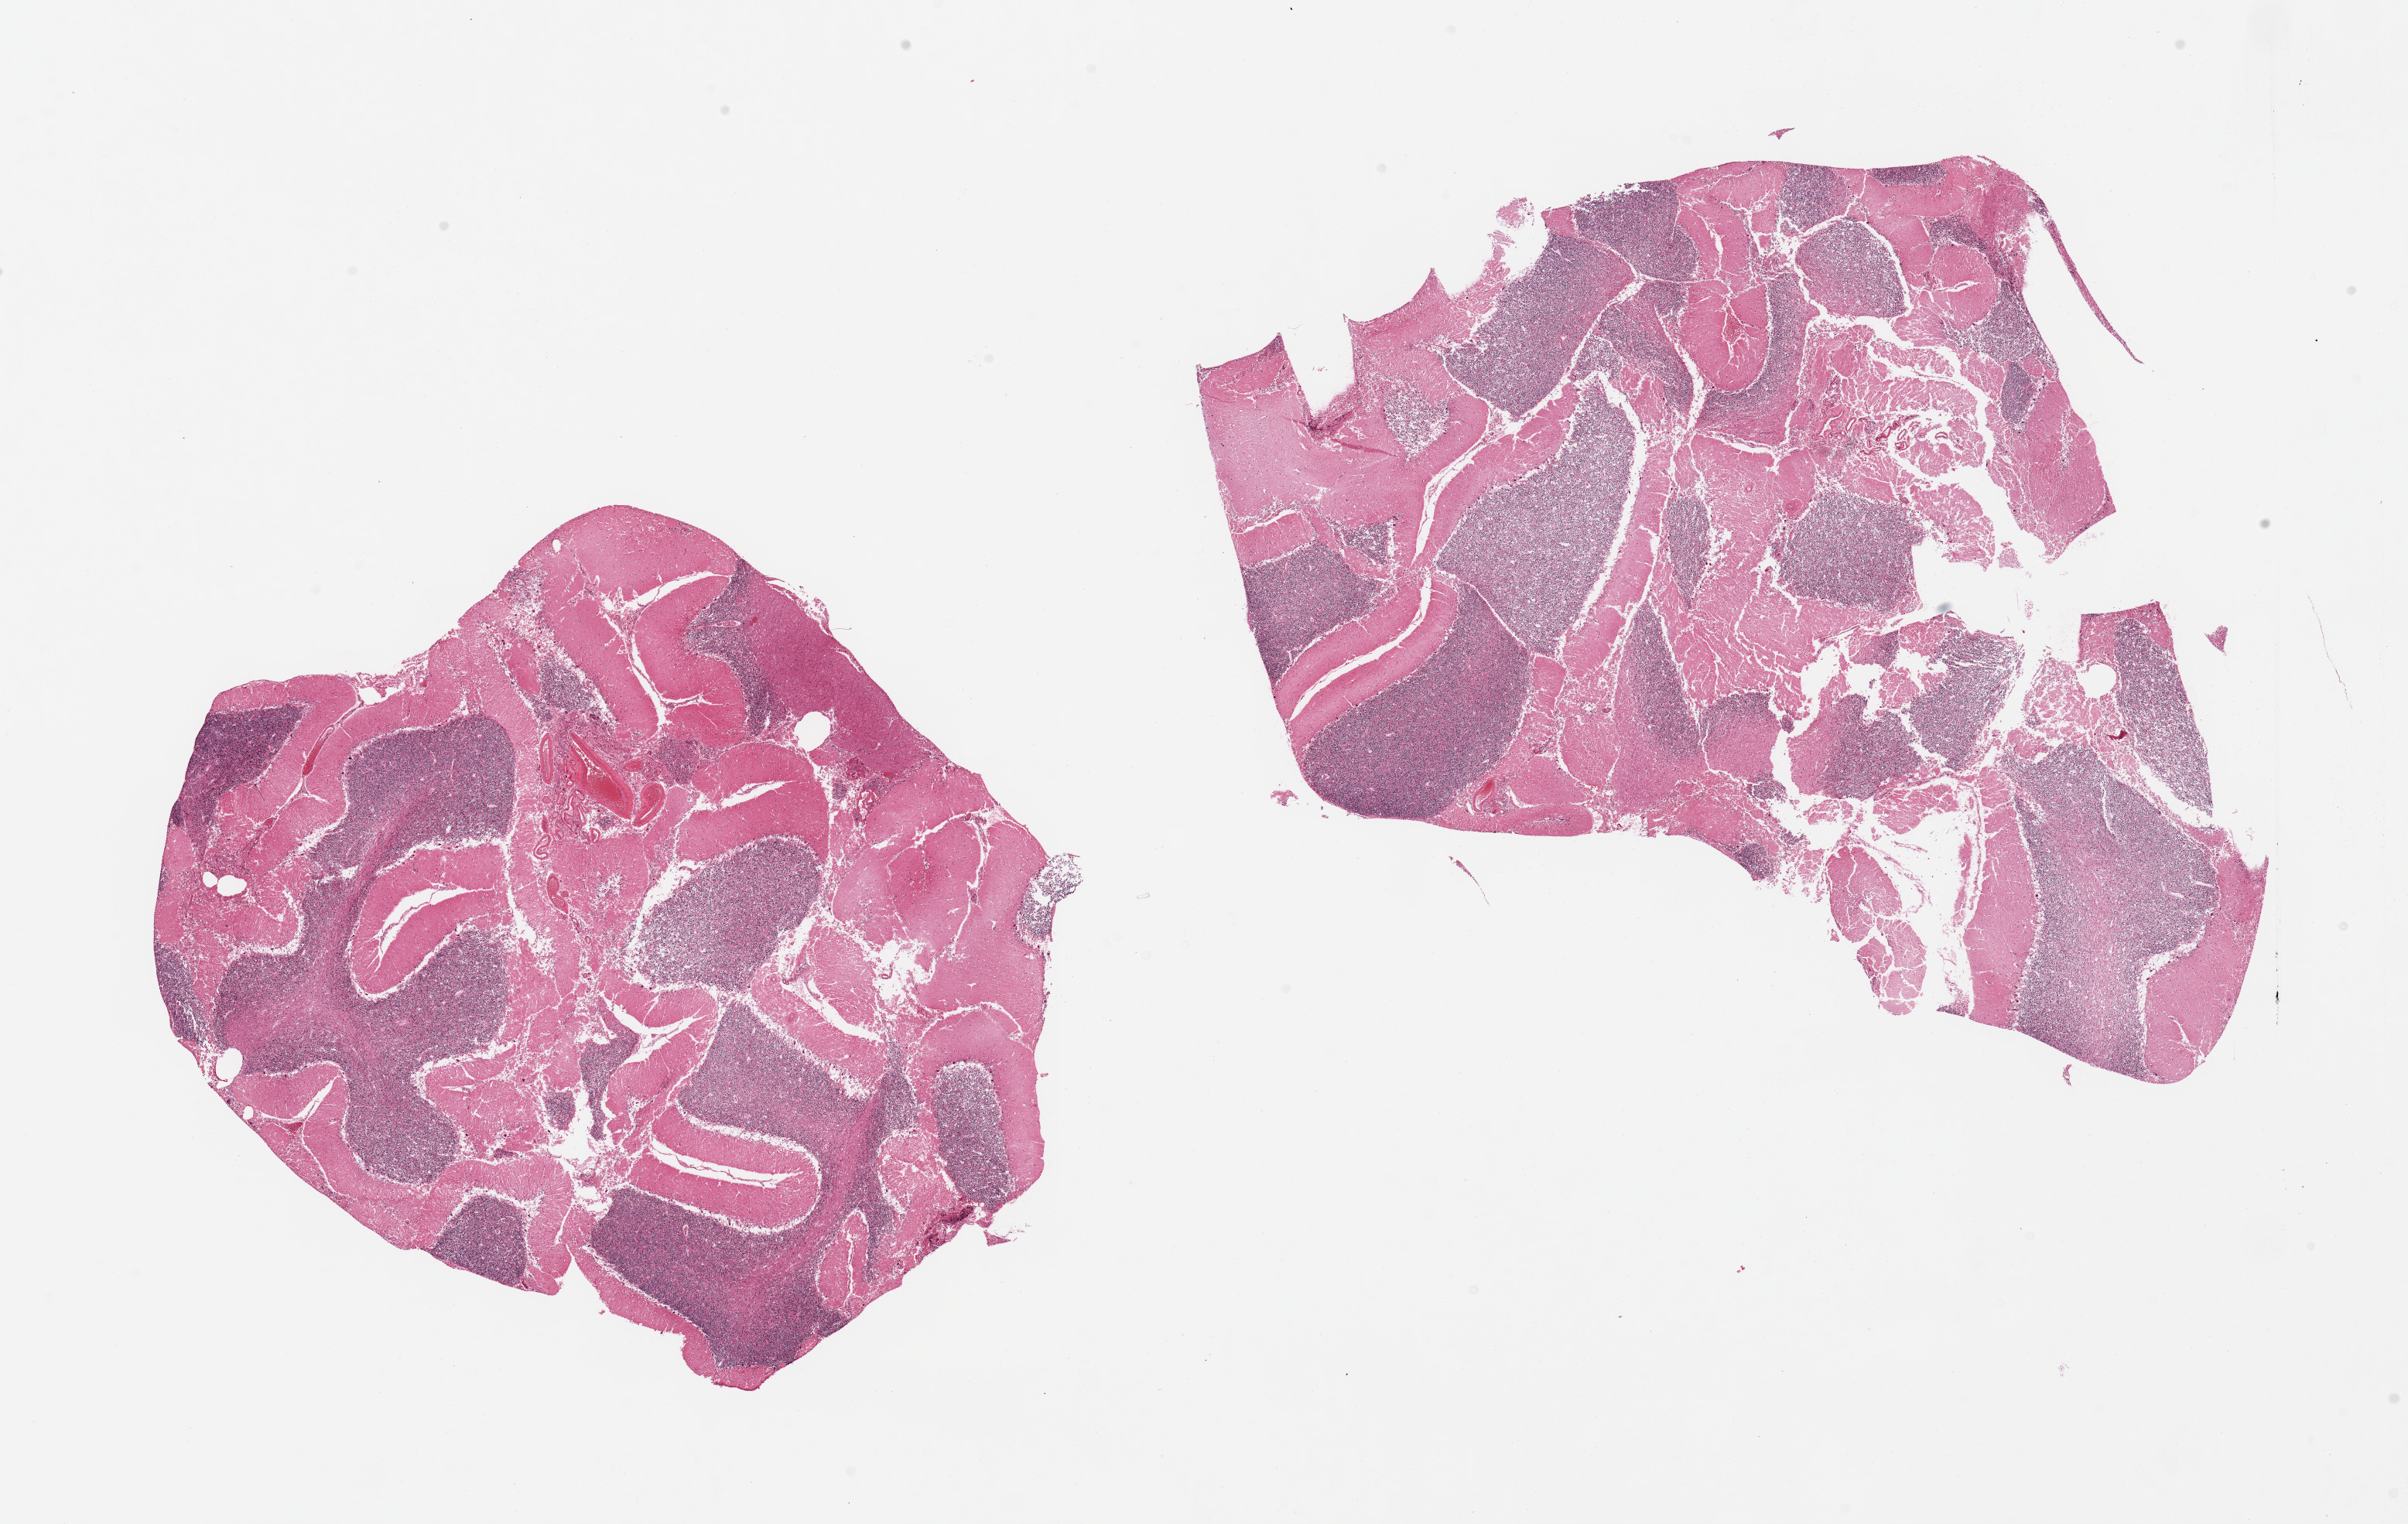
Hematoxylin and eosin (H&E) whole-slide image, low-resolution overview of the scanned area, about 24.6 x 15.6 mm (acquisition: 20x scan); PAXgene-fixed paraffin-embedded (PFPE) section; section of cerebellum (target tissue); donor tissue sample. Donor sex: male.
* review note (as recorded): 2 pieces, no abnormalities, poorly preserved